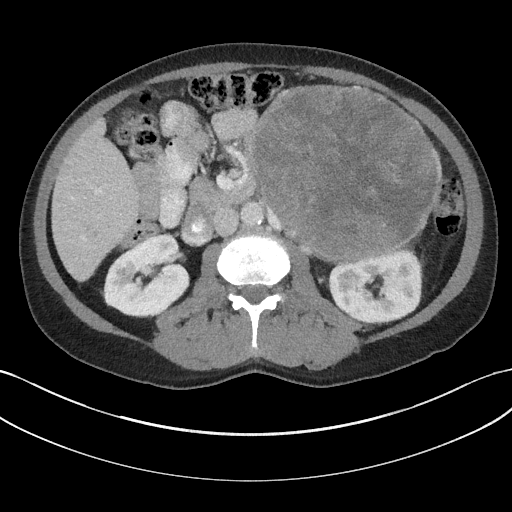
Contrast-enhanced abdominal CT, one axial slice. Slice 93 of 147 in the series (ordered by position). Reconstruction kernel I31f/3. 100 kVp. Soft-tissue window (W 400 / L 40 HU). 512 × 512 image matrix, field of view 384 × 384 mm. Patient: male, 58 years. From the clinical record (not read from this slice): diagnosis: adrenocortical carcinoma; tumour side: left adrenal; tumour size at pathology: 22 cm; Ki-67 index: 26 %; stage (as recorded): 2.
Outlined on this slice (semi-automatic segmentation, software-assisted and operator-edited):
- mass: bounding box (x1, y1, x2, y2) in pixels: (252, 87, 441, 259)